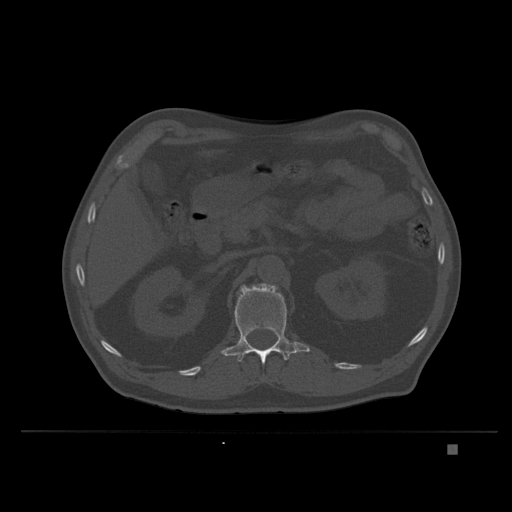
CT including the spine, one axial slice; position 139 of 435 along the scan axis; bone window (W 1800 / L 400 HU); 512 × 512 image matrix, field of view 434 × 434 mm. Patient: male, 73 years. Case-level facts recorded for this patient, not image findings: primary cancer: skin.
Structures marked on this image (semi-automatically segmented with operator editing):
- L1 vertebra: box from (x=221, y=283) to (x=310, y=365) px